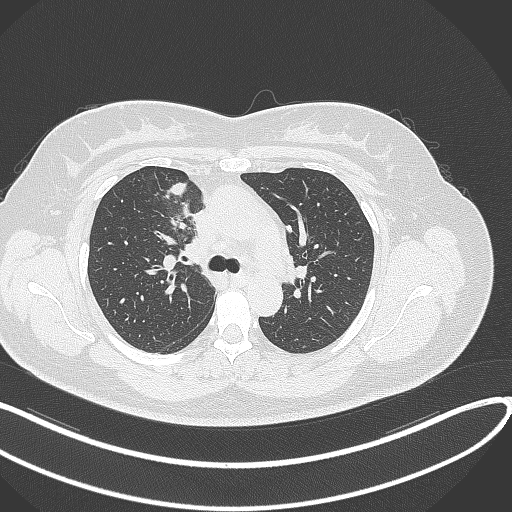
Chest CT, one axial slice. Position 190 of 303 along the scan axis. 120 kVp. Lung window (W 1500 / L -600 HU). 512 × 512 image matrix, field of view 400 × 400 mm. Female patient, age 46 years. From the clinical record (not read from this slice): clinical TNM (as recorded): T2a N1 M0.
Structures marked on this image (rectangle marked by the reading radiologist):
- lung tumour (recorded histology: adenocarcinoma): bounding box (x1, y1, x2, y2) in pixels: (163, 177, 194, 220)